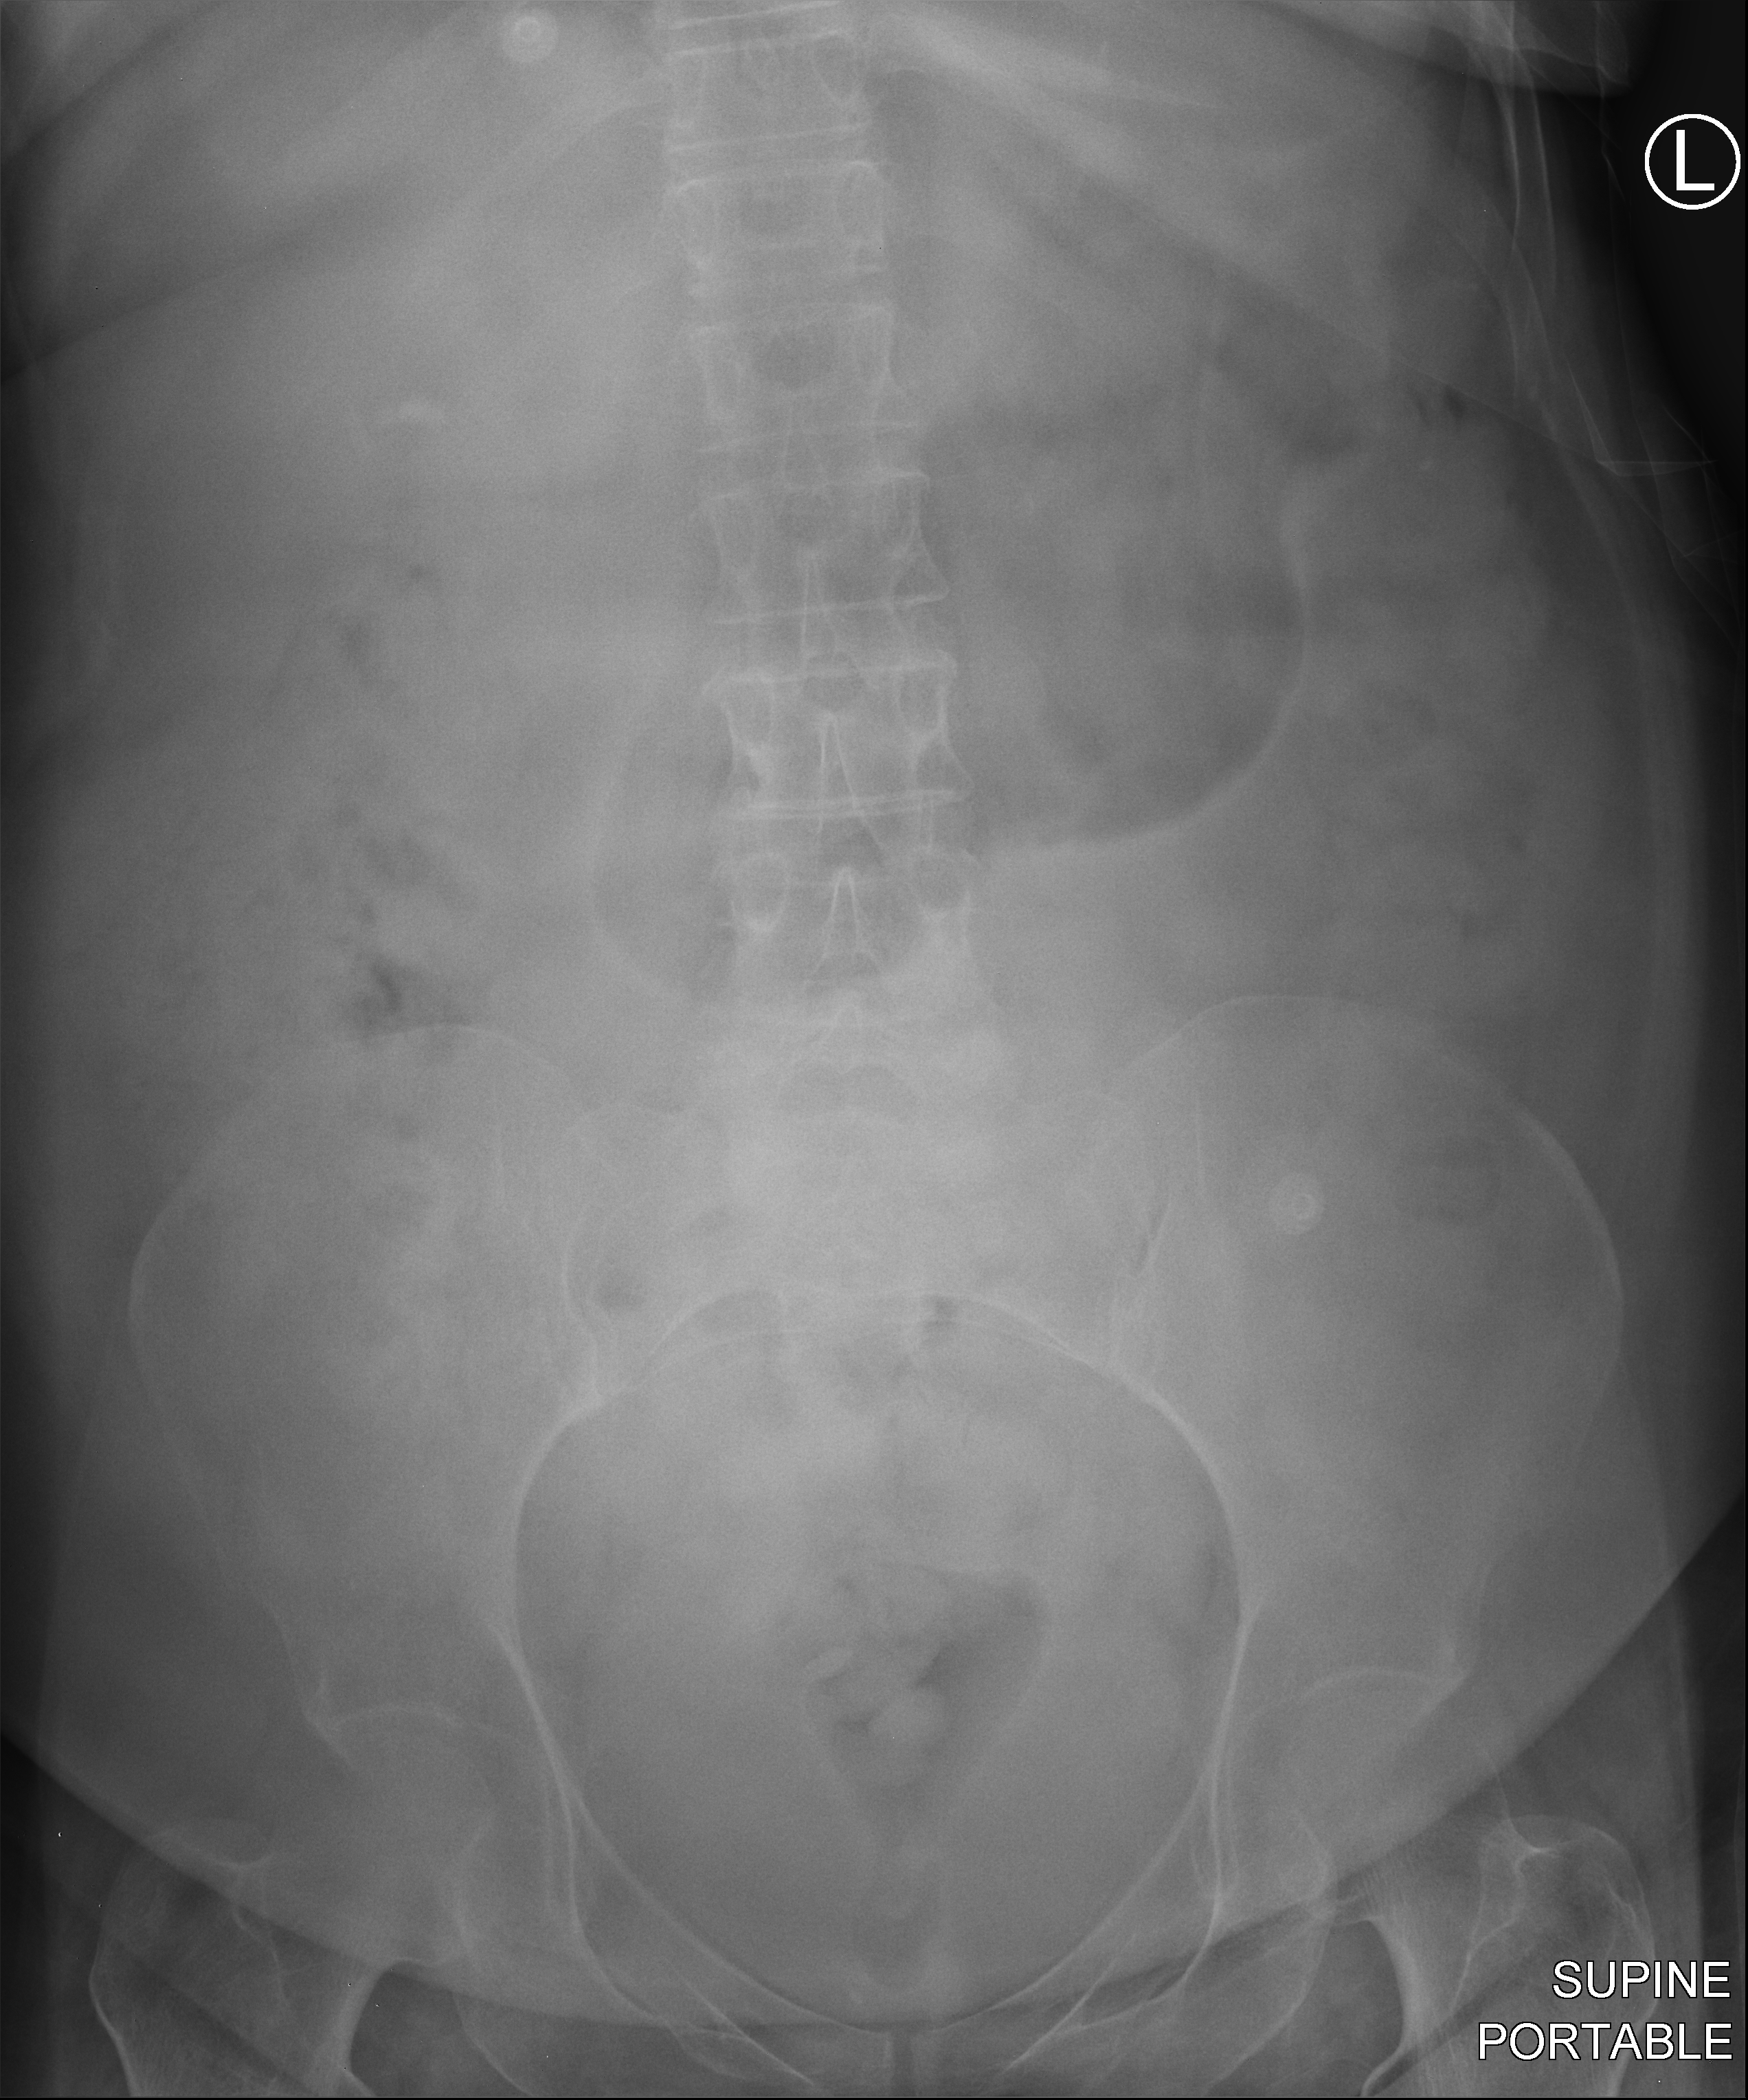
Portable abdomen radiograph. Patient hospitalised with COVID-19; female, aged 18–59 years.
Admission-level facts for this patient (not findings on this image; timing relative to this image not recorded): length of hospital stay: 44 days.